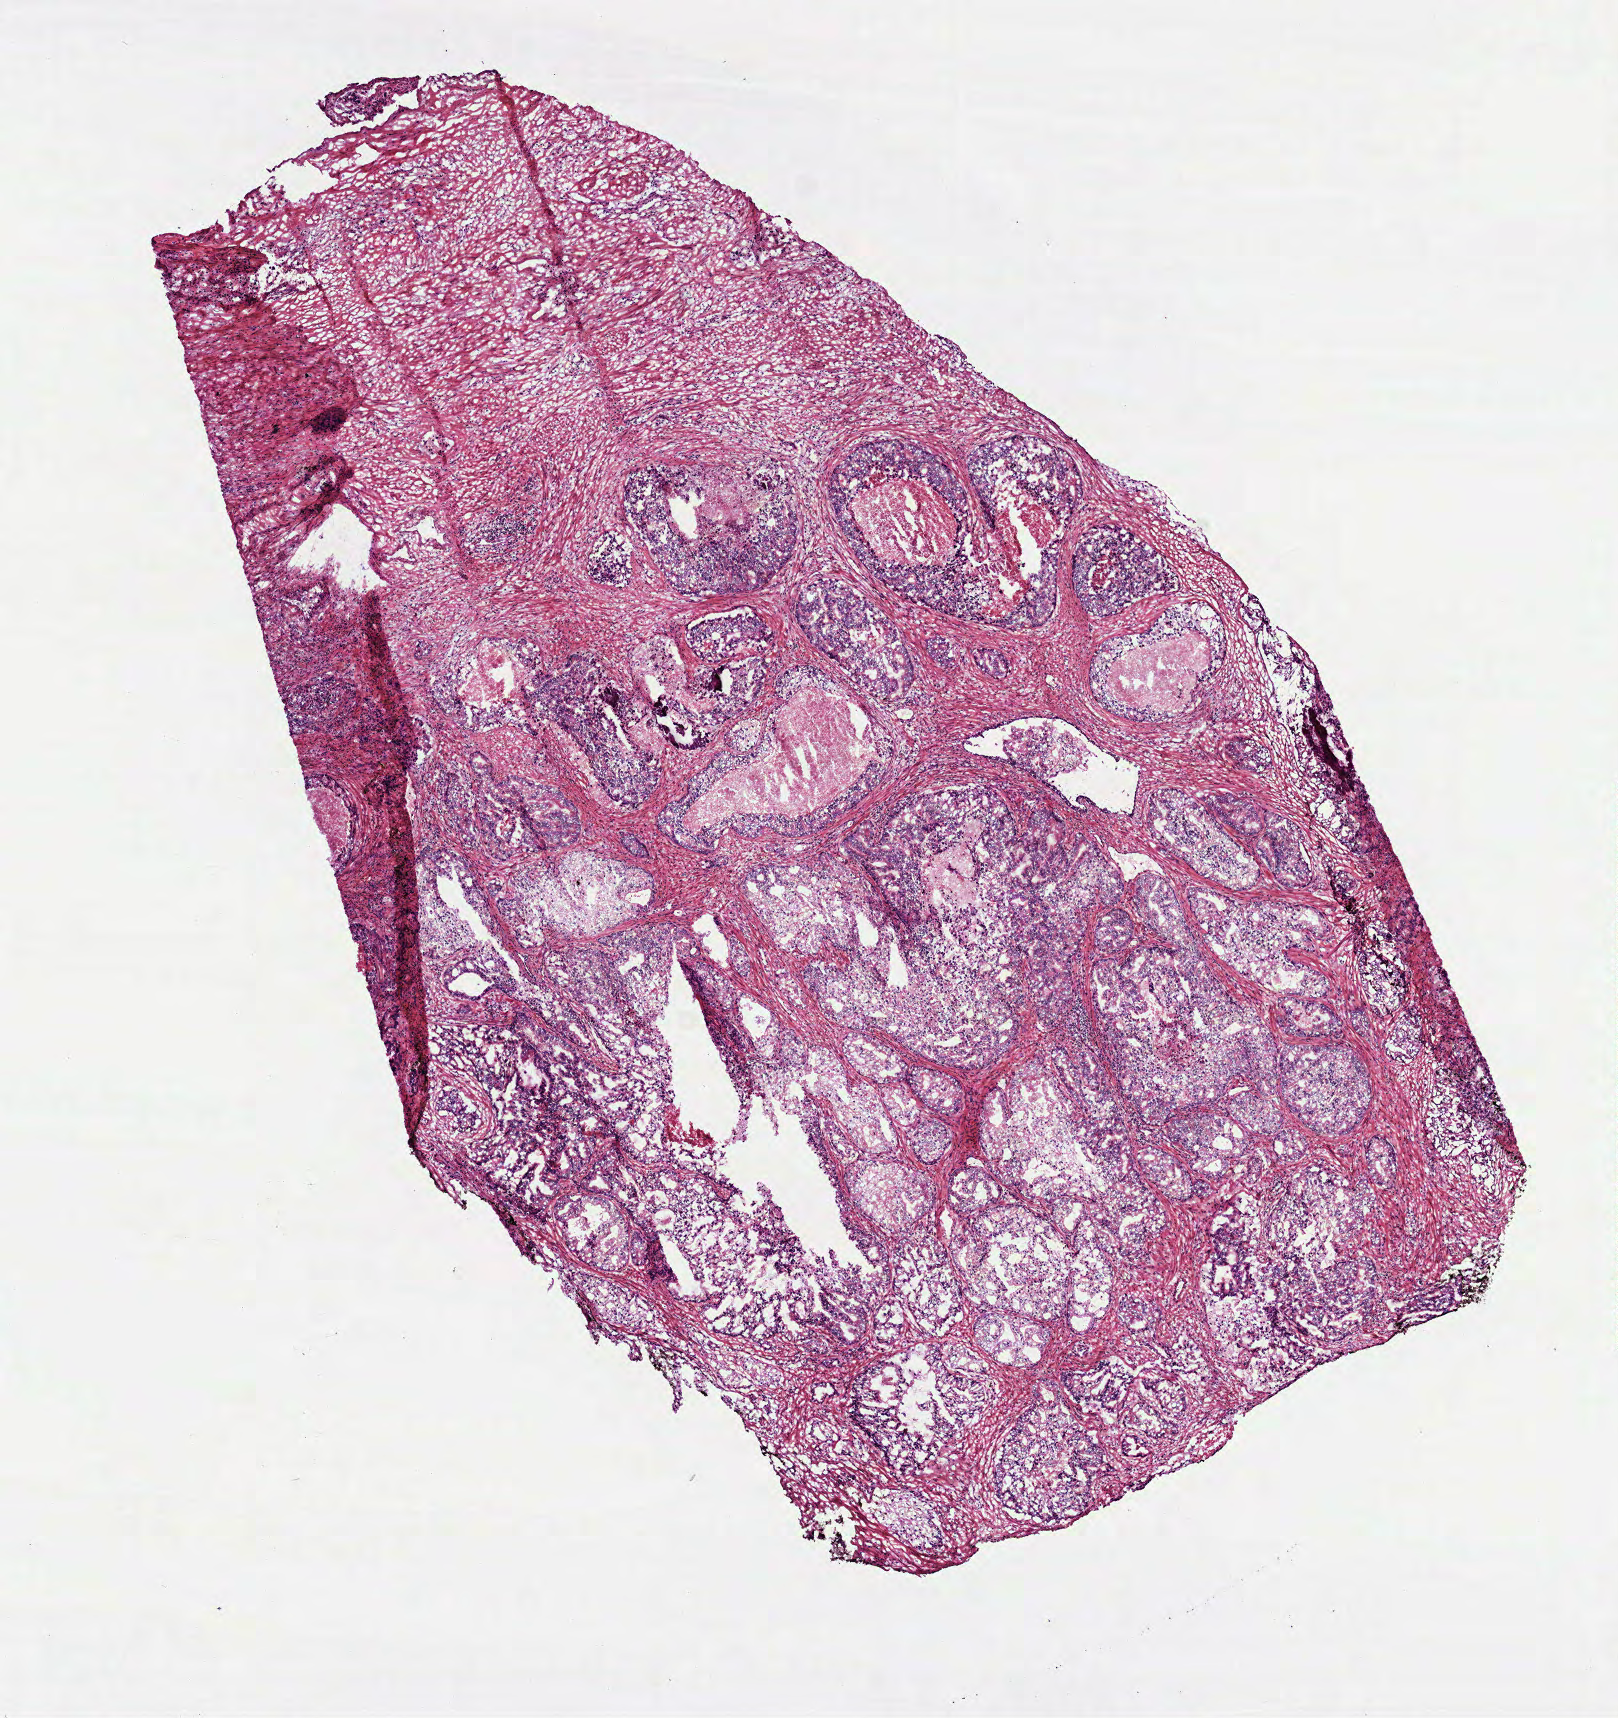
Digitized H&E tissue section (whole slide), low-resolution overview of the scanned area, about 6.5 x 6.9 mm (acquisition: 40x scan); frozen section; prostate, primary tumour sample. Patient: male, age at initial diagnosis 58 years. Gleason score: 9 (5+4). Composition of this section per pathologist review: tumour cells 60%, tumour nuclei 80%, normal cells 0%, stromal cells 35%, necrosis 5%. Infiltration values recorded for this section: lymphocyte infiltration 0%, monocyte infiltration 0%, neutrophil infiltration 0%.
Diagnosis: Adenocarcinoma, NOS.